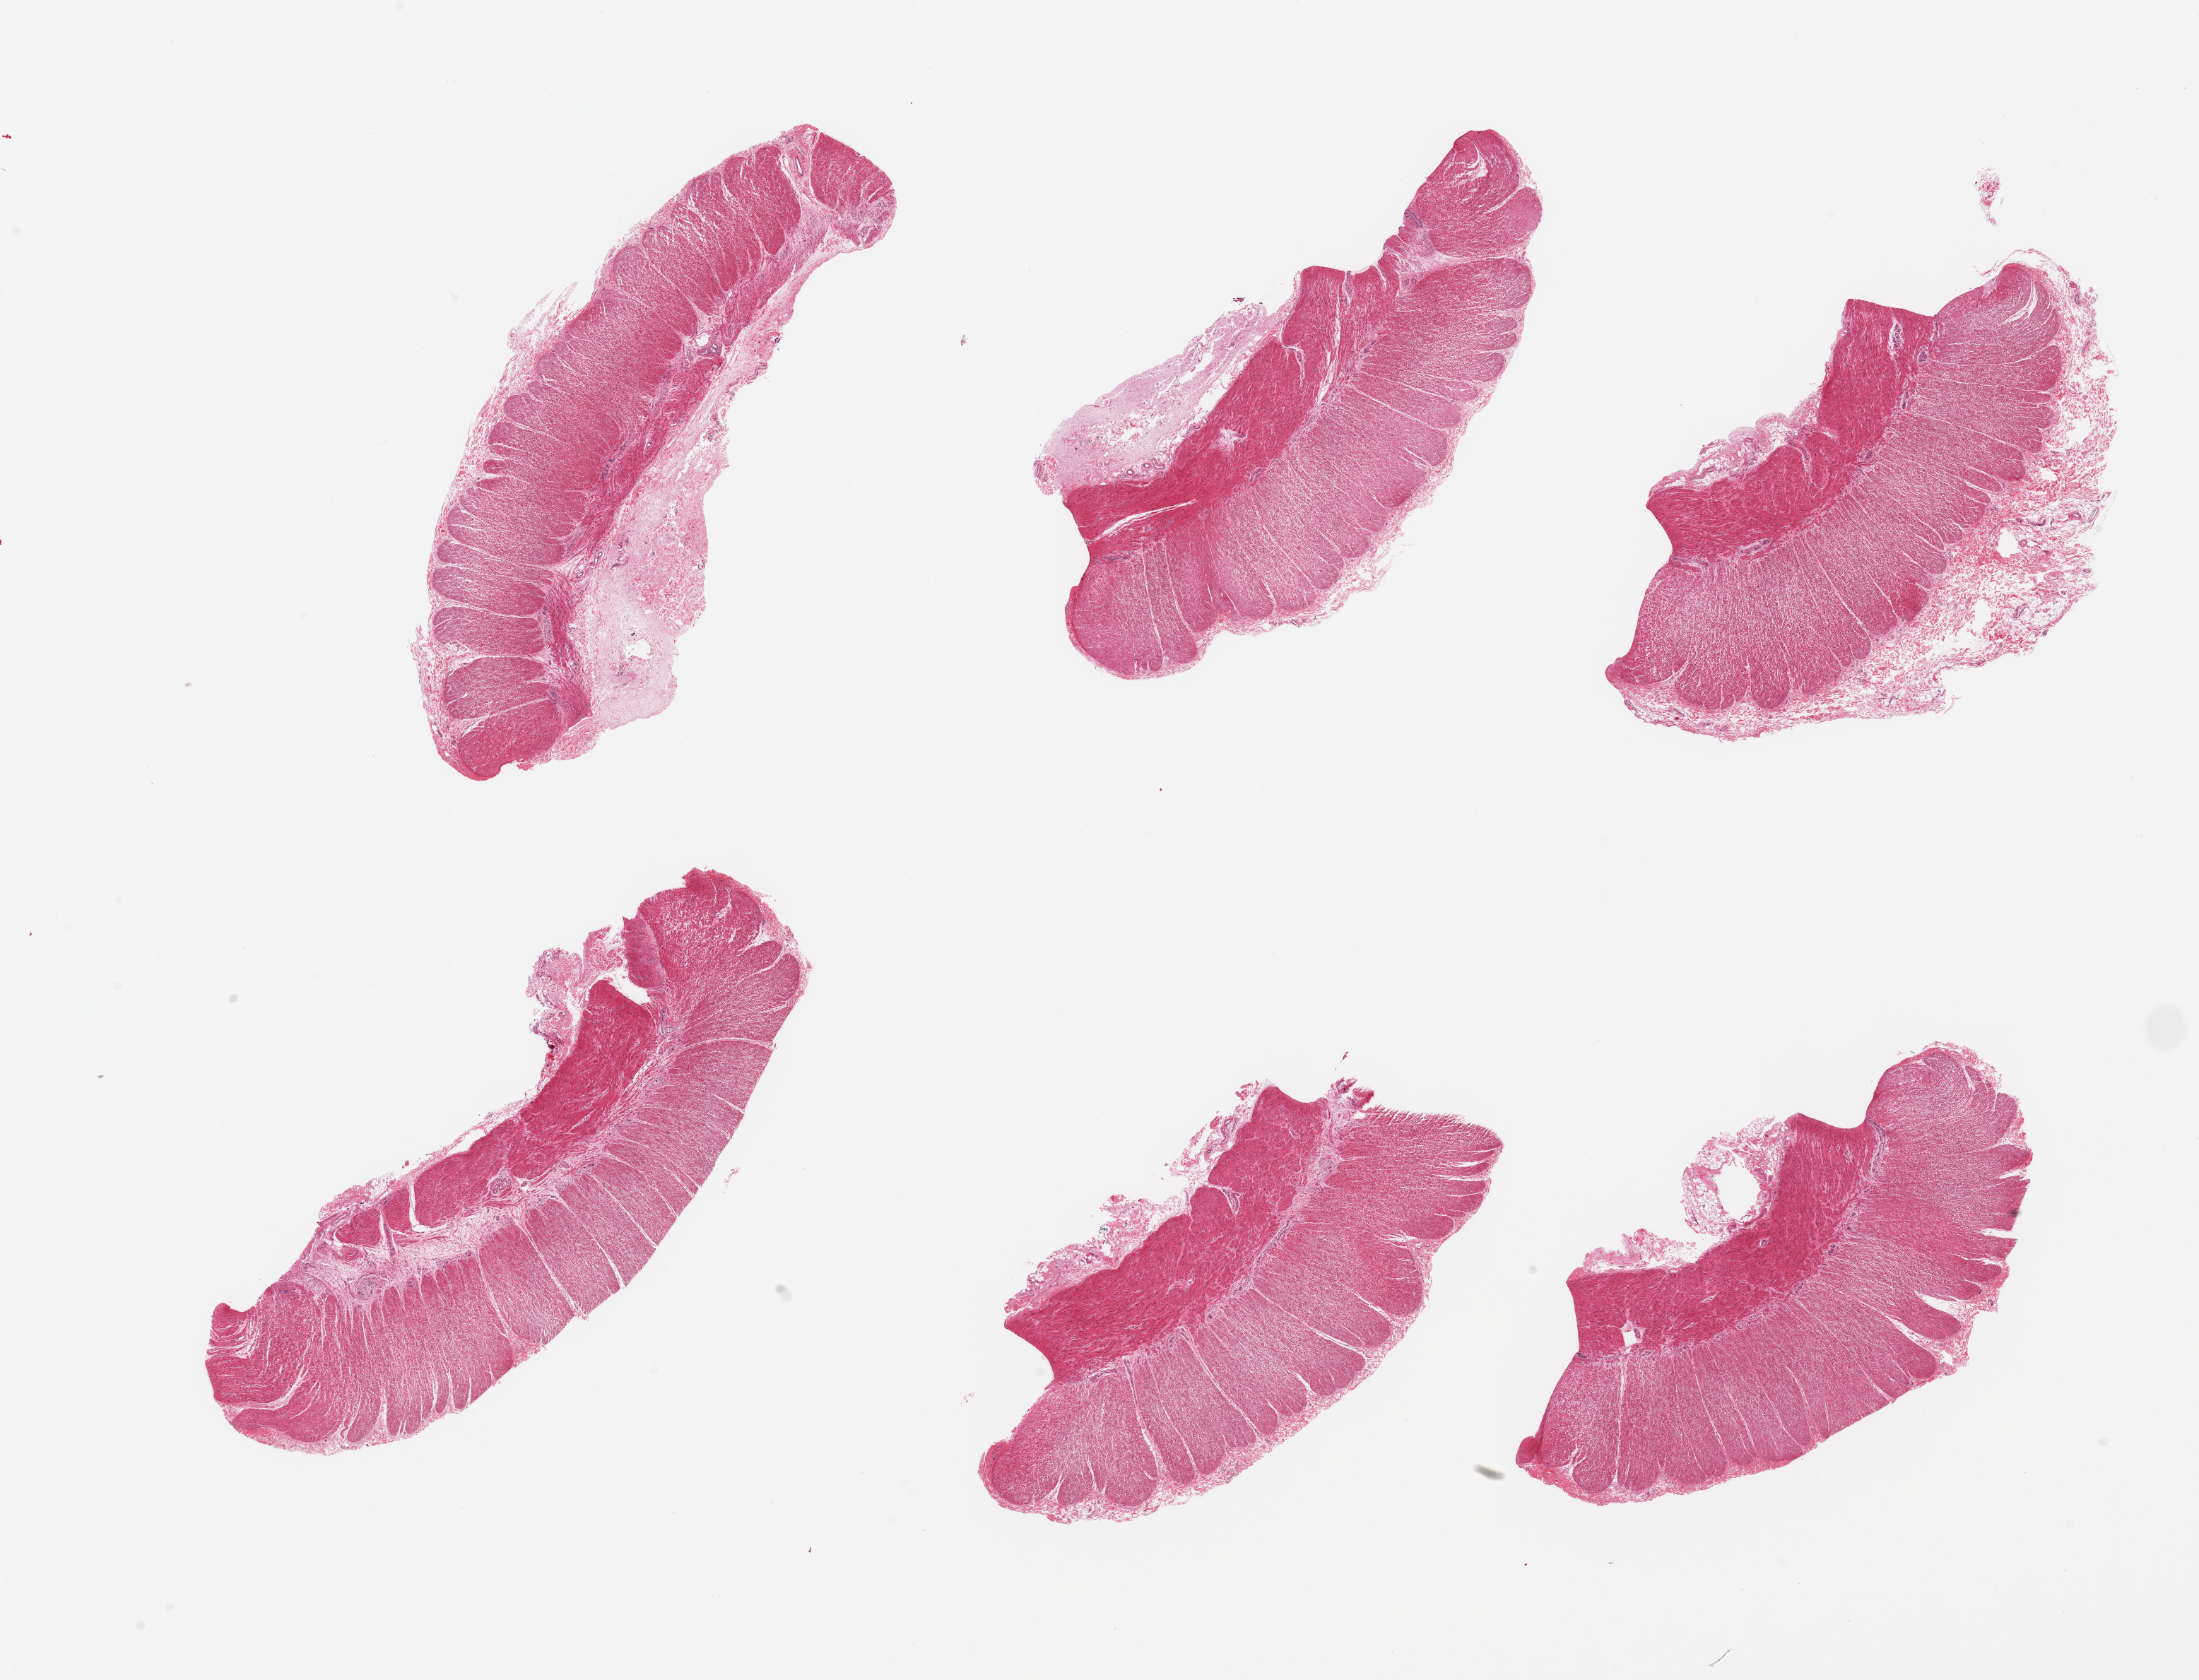
Haematoxylin and eosin whole-slide image — low-resolution overview of the scanned area, about 24.6 x 18.8 mm. PAXgene-fixed paraffin-embedded (PFPE) section. Target tissue: sigmoid colon. Donor tissue sample.
Pathologist's review note for this sample: 6 pieces; target muscularis.